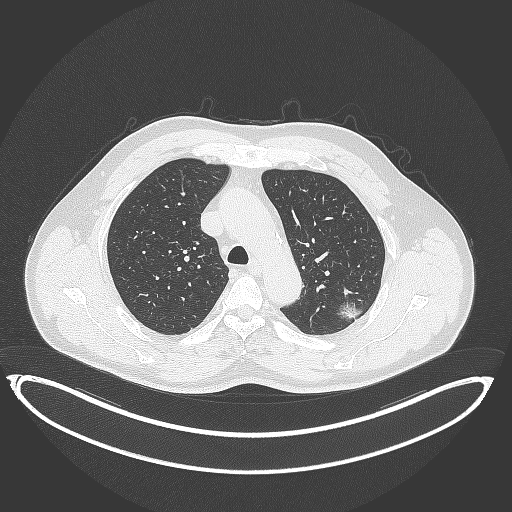
Chest CT, one axial slice. Position 266 of 399 along the scan axis. Reconstruction kernel B70f. 120 kVp. Lung window (W 1500 / L -600 HU). 512 × 512 image matrix, field of view 469 × 469 mm. Male patient, age 58 years. Case-level facts recorded for this patient, not image findings: clinical TNM (as recorded): T1c N0 M0; histopathological grade: G1-2.
Outlined on this slice (bounding box drawn by a radiologist):
- lung tumour (recorded histology: adenocarcinoma): bounding box [x1, y1, x2, y2] px = [337, 301, 364, 323]